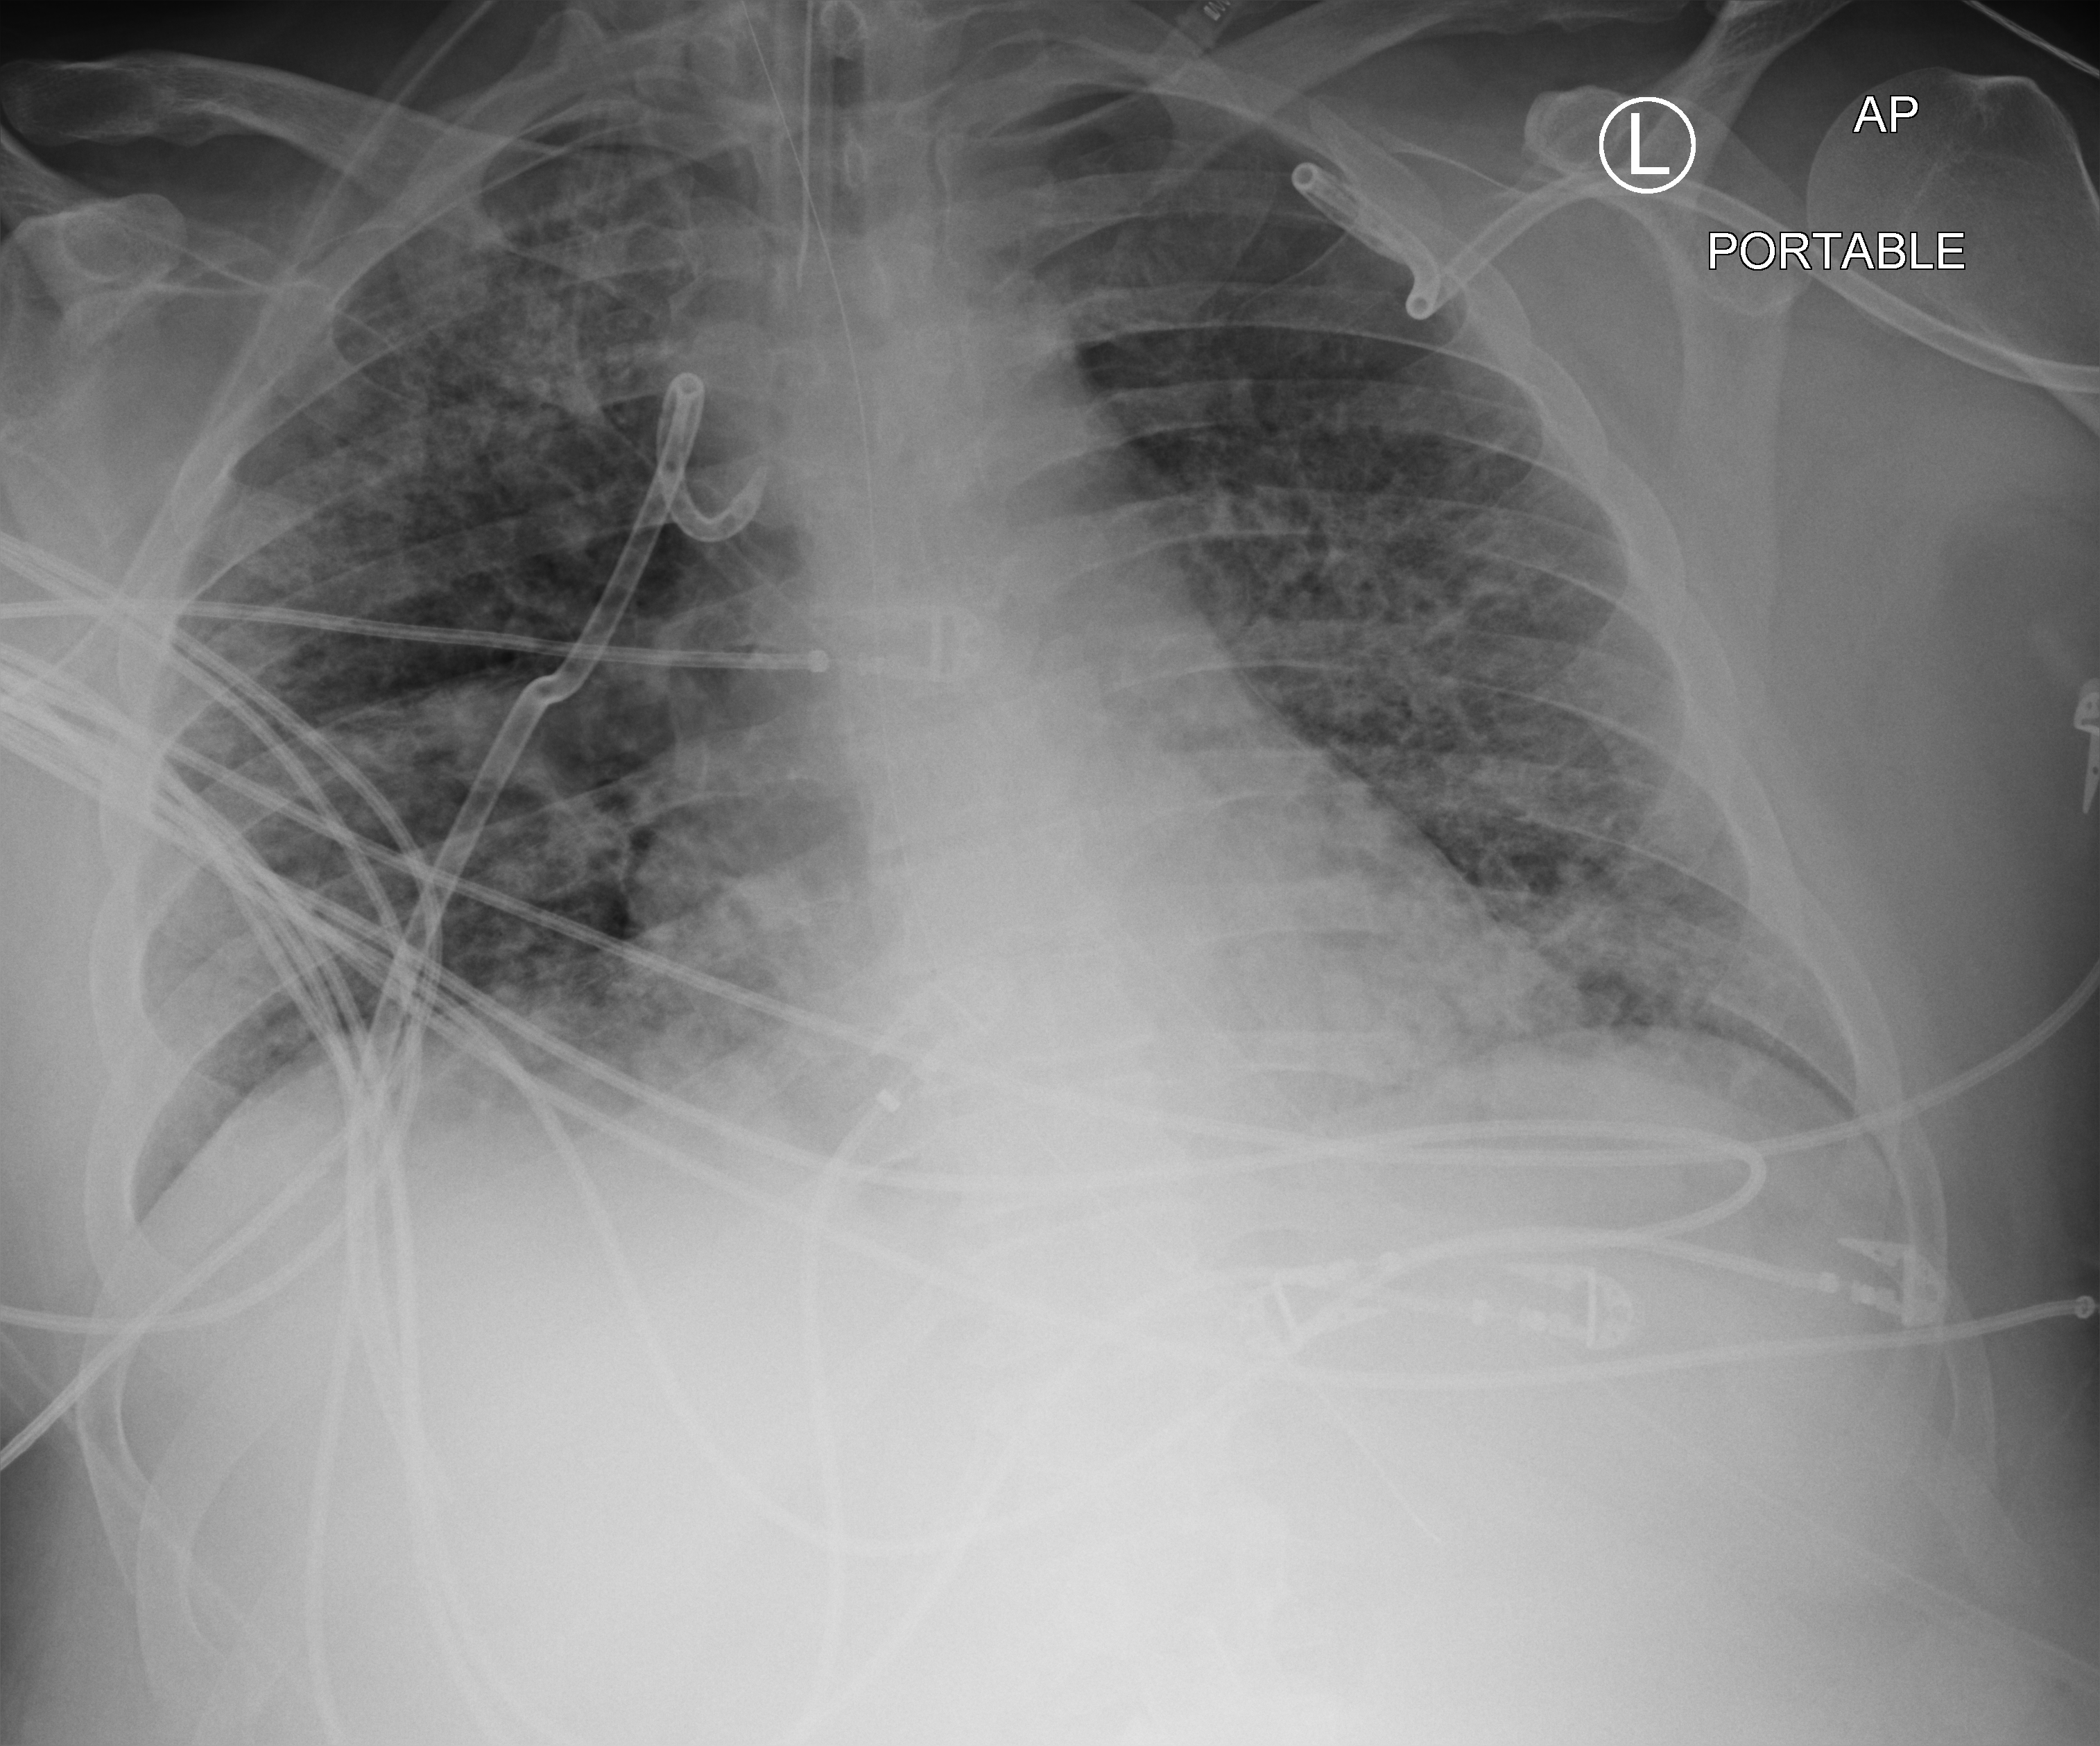
Chest X-ray (portable); anteroposterior (AP) projection. Adult patient hospitalised with COVID-19, age 18–59 years.
Admission-level facts for this patient (not findings on this image; timing relative to this image not recorded): admitted to intensive care during this hospital stay: yes.